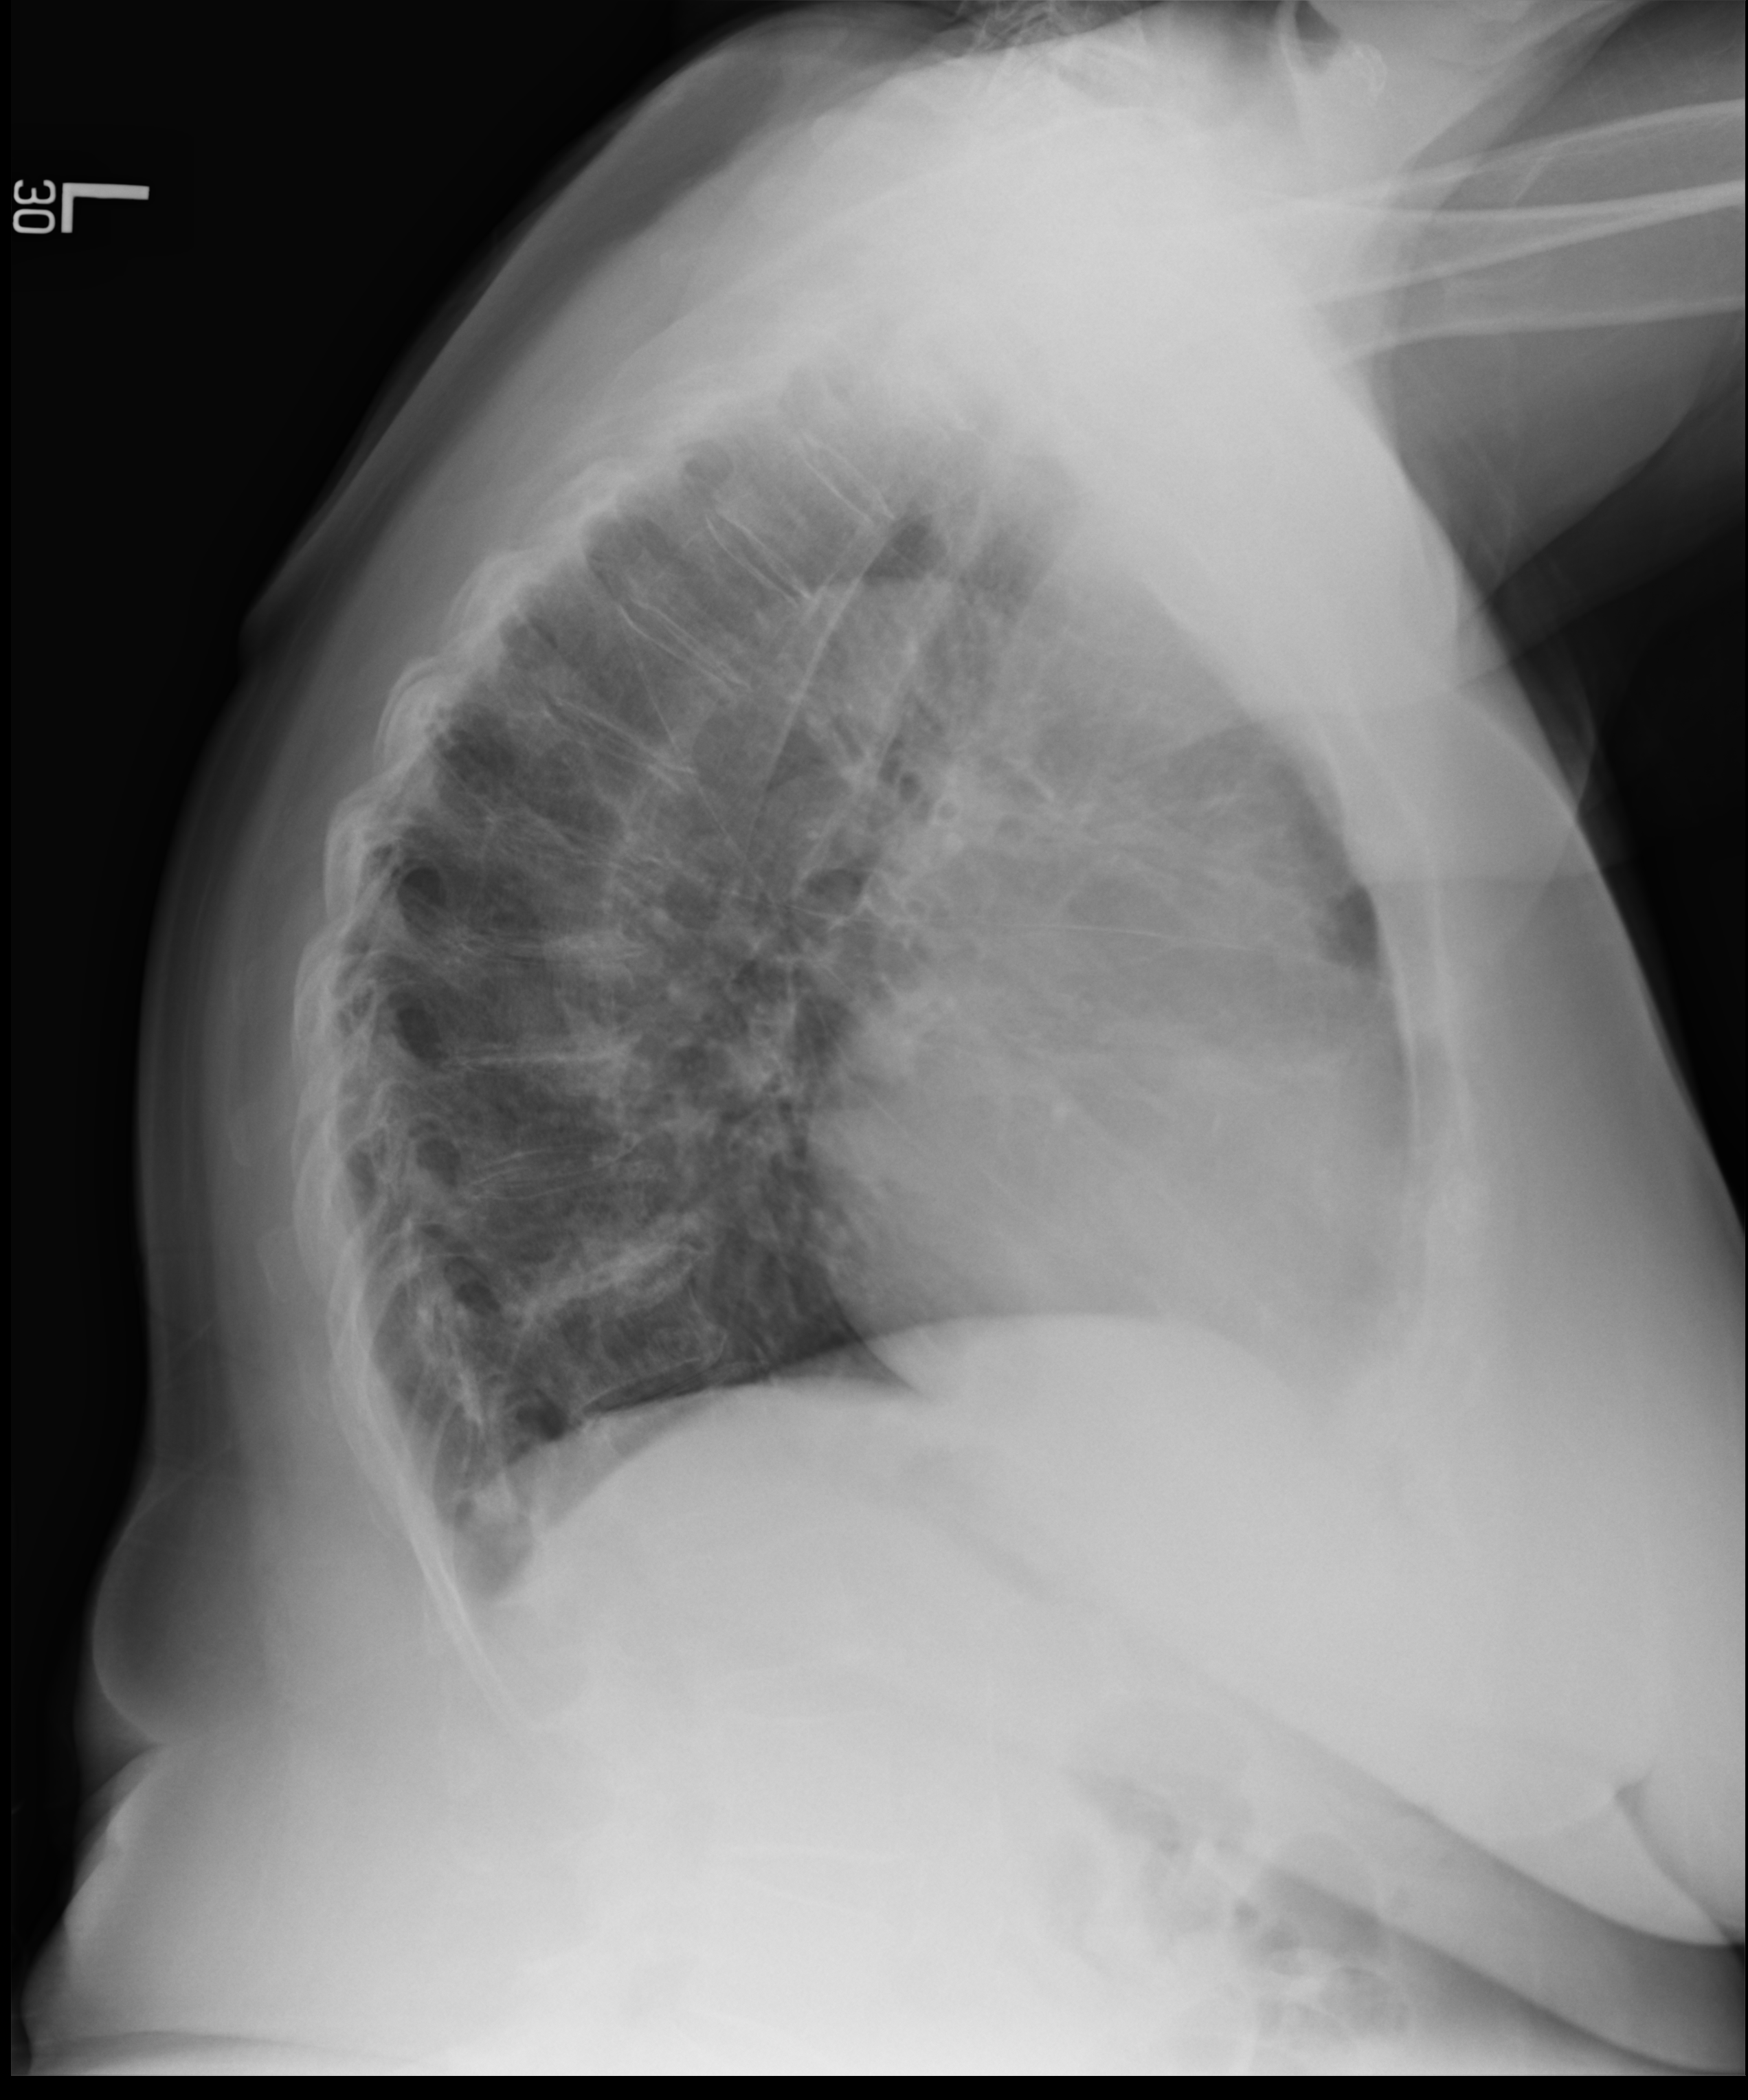
Chest radiograph; lateral projection. Female patient hospitalised with COVID-19, age 75–90 years.
From the hospital-stay record, not from the radiograph (when in the stay this image was taken is not recorded):
- mechanically ventilated during this hospital stay: no